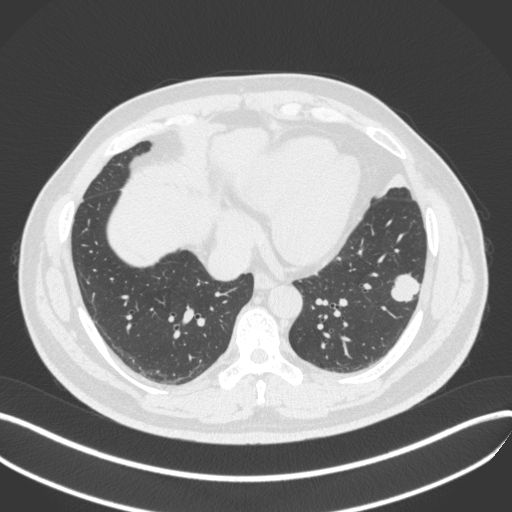
Chest CT, one axial slice. Reconstruction kernel B31f. 120 kVp. Lung window (W 1500 / L -600 HU). 1 mm slice thickness. 512 × 512 image matrix, field of view 400 × 400 mm. Male patient, age 39 years. Case-level facts recorded for this patient, not image findings: clinical TNM (as recorded): T2a N0 M0.
Annotated regions visible in this slice (rectangle marked by the reading radiologist):
- lung tumour (recorded histology: adenocarcinoma): bounding box [x1, y1, x2, y2] px = [387, 270, 425, 305]